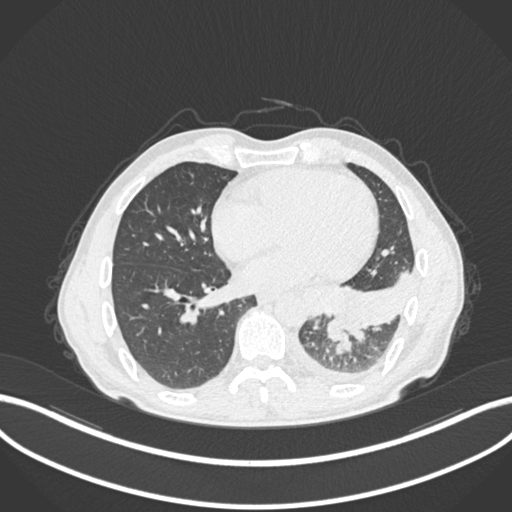
Chest CT, one axial slice; slice 93 of 222 in the series (ordered by position); reconstruction kernel B30f; 120 kVp; lung window (W 1500 / L -600 HU); 1 mm slice thickness; 512 × 512 image matrix. Male patient, age 47 years. Case-level facts recorded for this patient, not image findings: clinical TNM (as recorded): T3 N1 M1c; histopathological grade: G3.
Annotated regions visible in this slice (bounding box drawn by a radiologist):
- lung tumour (recorded histology: small cell carcinoma): box from (x=322, y=314) to (x=348, y=347) px